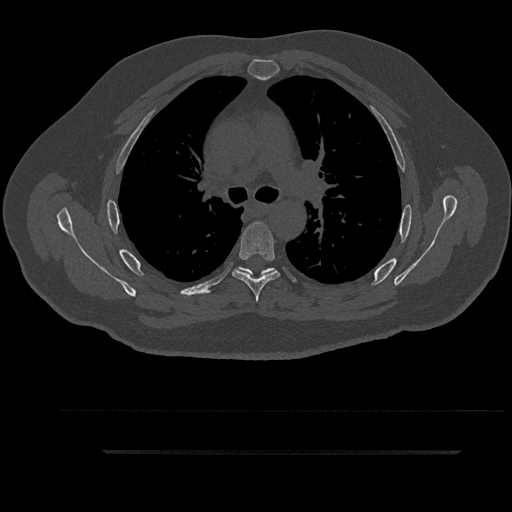
CT including the spine, one axial slice; reconstruction kernel Br40s/3; 120 kVp; bone window (W 1800 / L 400 HU); 0.5 mm slice thickness; 512 × 512 image matrix, field of view 432 × 432 mm. Patient: male, 63 years. From the clinical record (not read from this slice): primary cancer: renal; vertebrae with lytic lesions (as recorded): T8.
Outlined on this slice (semi-automatically segmented with operator editing):
- T5 vertebra: box from (x=232, y=222) to (x=280, y=302) px
- T6 vertebra: (x=238, y=267)–(x=276, y=279)